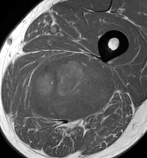
MRI of an extremity soft-tissue mass, one axial slice; slice 69 of 86 in the series (ordered by position); MR volume resampled by the dataset authors to the PET/CT grid (not the native acquisition matrix); 147 × 158 image matrix, field of view 144 × 154 mm. Male patient. Case-level facts recorded for this patient, not image findings: histological type: undifferentiated pleomorphic liposarcoma; grade: high; site of the primary tumour: left thigh.
Structures marked on this image (expert contour drawn on MRI and transferred to this co-registered scan by the dataset authors):
- gross tumour volume including surrounding oedema: bounding box <19,56,115,127> (left, top, right, bottom; pixels)
- gross tumour volume (mass): <30,58,113,118>